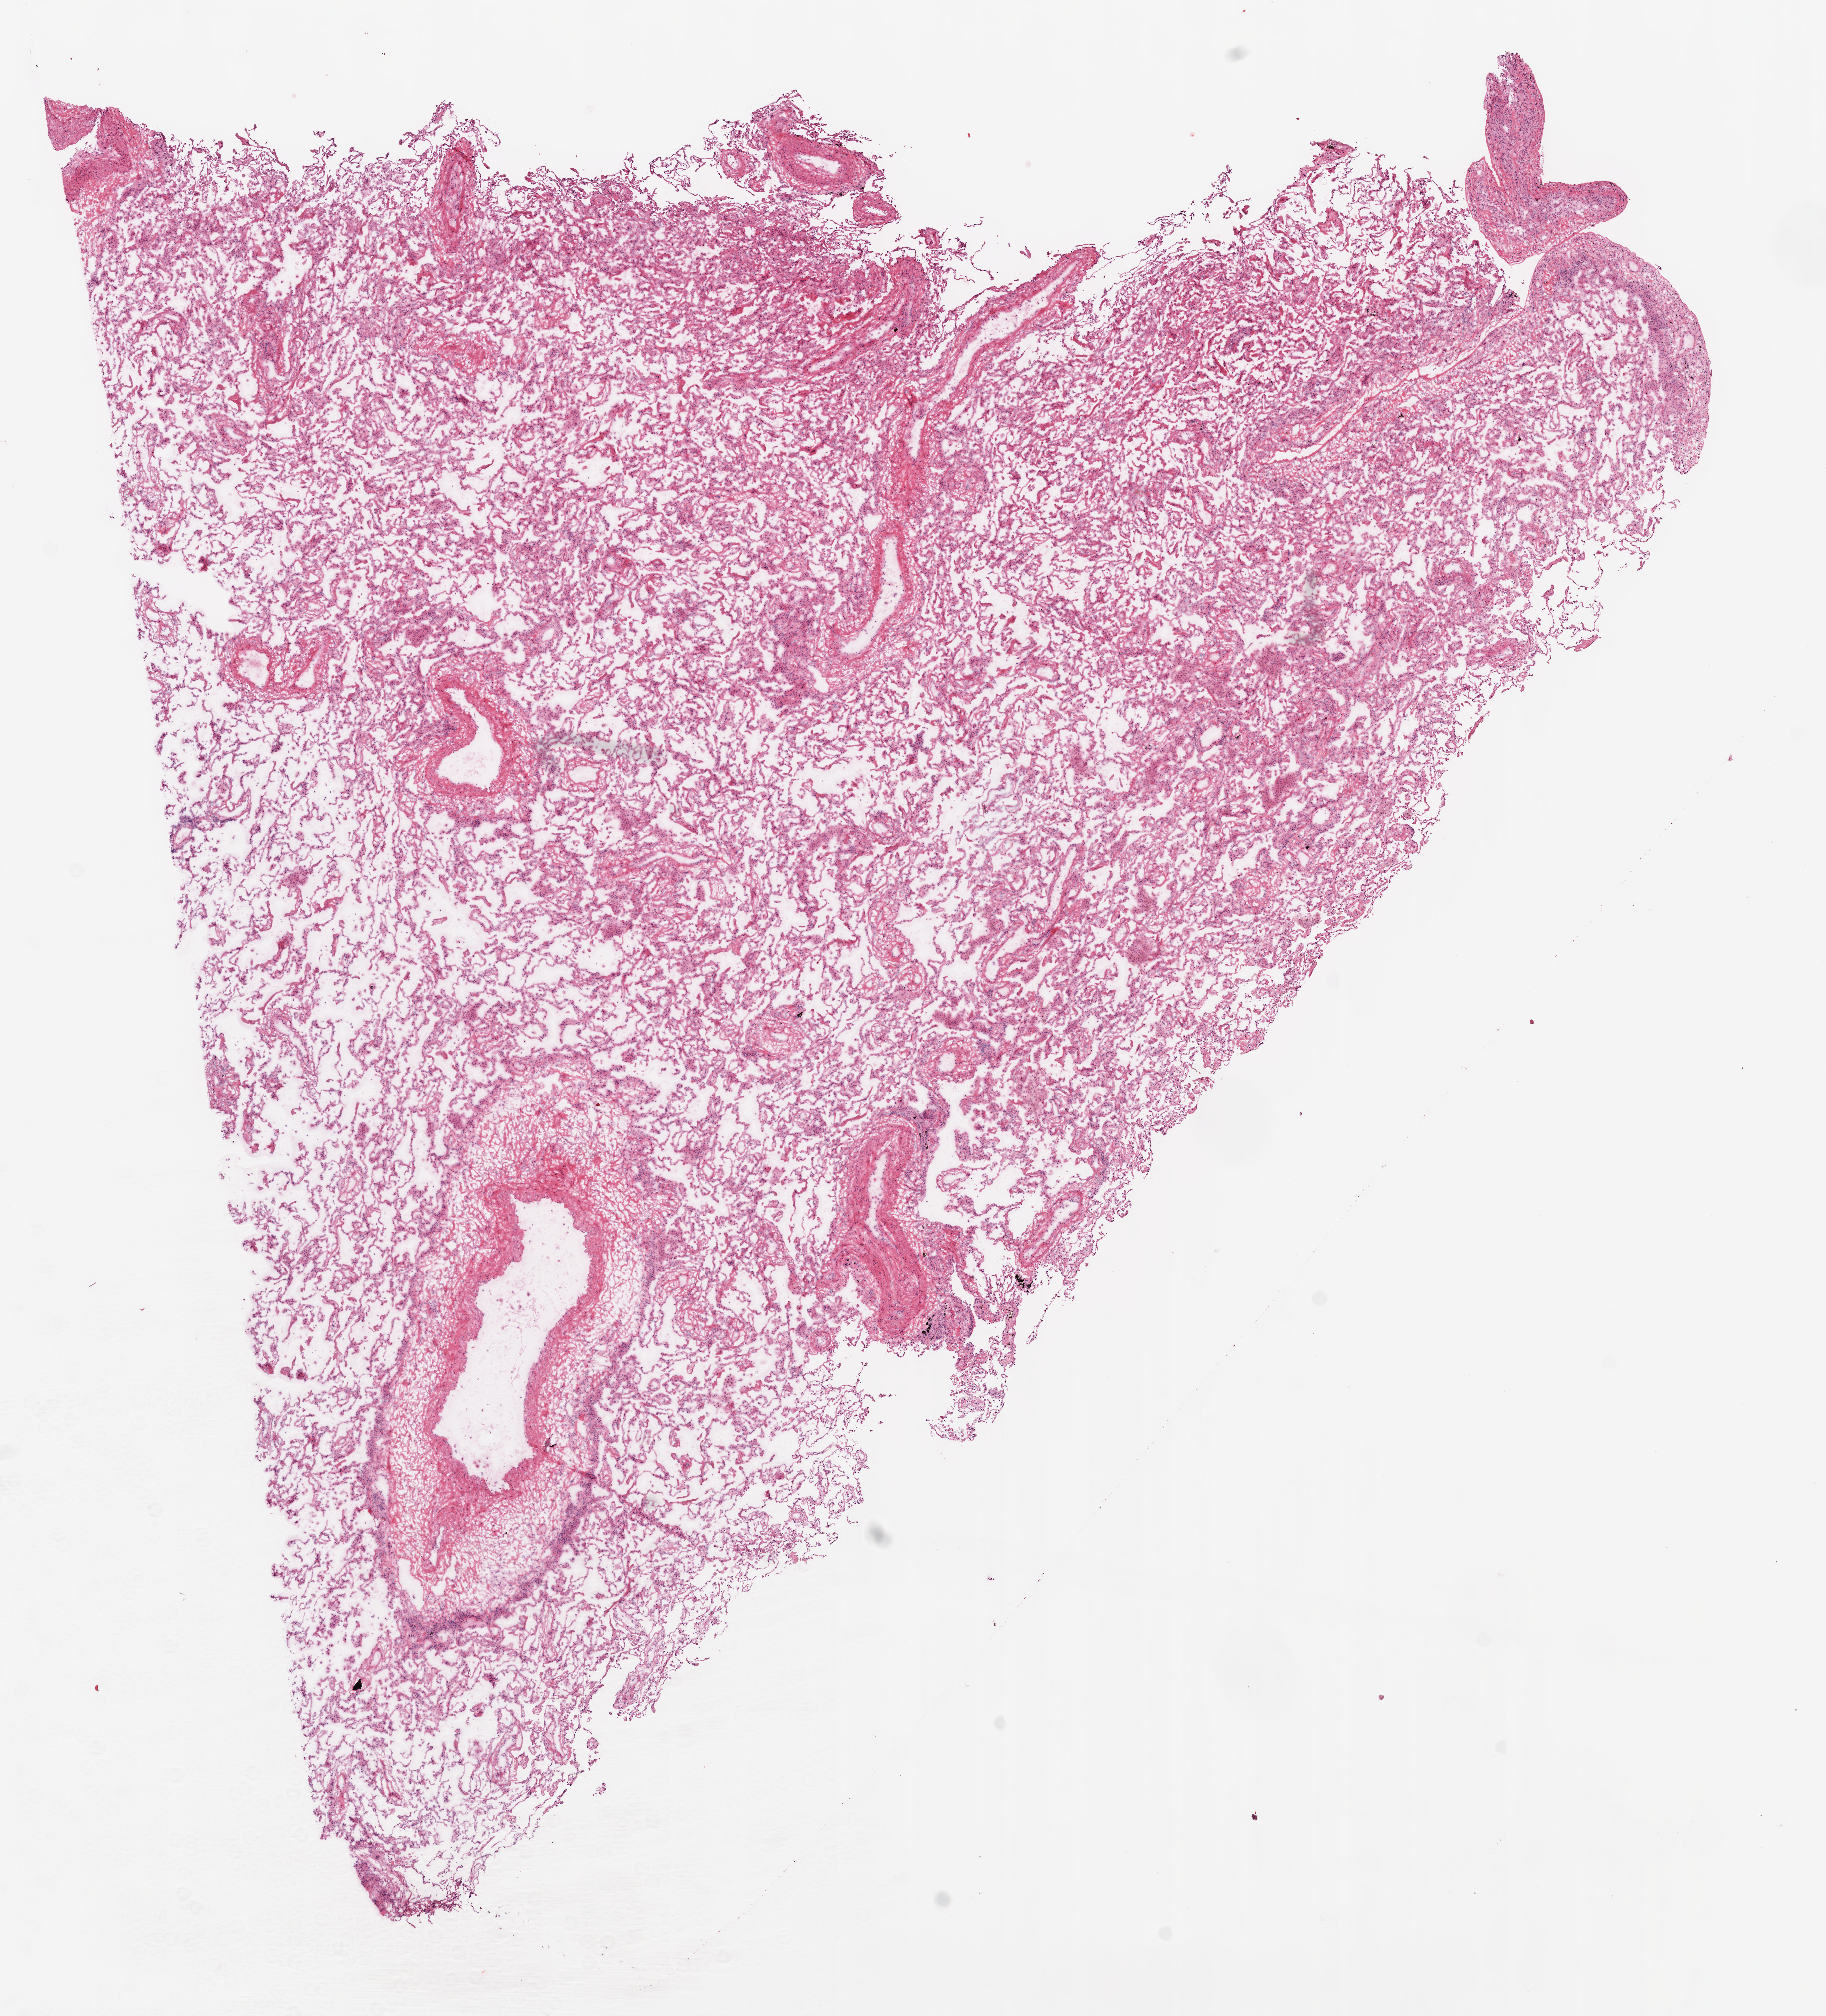
Digitized Hematoxylin and eosin (H&E) stained tissue section (whole slide) — shown as a low-resolution overview of the whole scanned area (about 11.0 x 12.2 mm, from a 20x scan); frozen section; sample: solid tissue normal (non-tumour tissue), lung. Male, age 73 years at initial diagnosis.
* this section: solid tissue normal sample (biorepository sample class)
* patient diagnosis: Squamous cell carcinoma, NOS